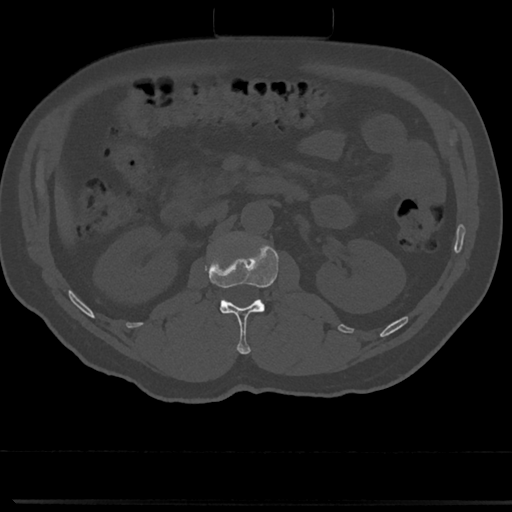
CT including the spine, one axial slice. Slice 66 of 817 in the series (ordered by position). Reconstruction kernel Br40s/3. 120 kVp. Bone window (W 1800 / L 400 HU). 0.5 mm slice thickness. 512 × 512 image matrix. Male patient, age 61 years. Case-level facts recorded for this patient, not image findings: primary cancer: prostate.
Structures marked on this image (semi-automatic segmentation, software-assisted and operator-edited):
- L1 vertebra: bounding box [x1, y1, x2, y2] px = [205, 235, 300, 354]